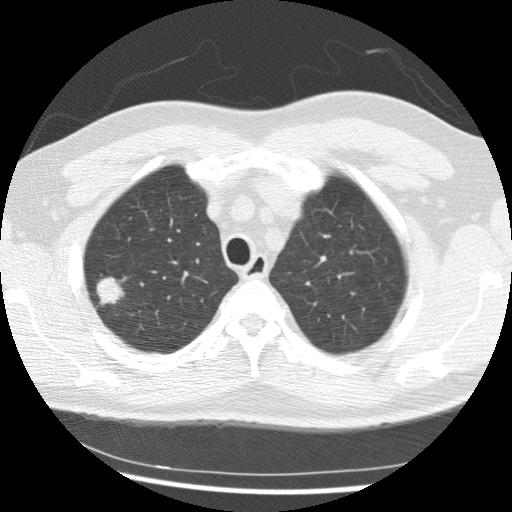
Low-dose screening chest CT, axial slice. First (baseline) screen. Lung window (W 1500 / L -600 HU). 512 × 512 image matrix. Male, age 56 years at enrolment. Current smoker at enrolment.
- Expert reader's lesion annotation, bounding box [x1, y1, x2, y2] px = [81, 272, 131, 315].
- Screening reader's record for this exam (one nodule recorded; not confirmed to be the boxed lesion): non-calcified nodule or mass ≥4 mm, right upper lobe, 19 × 15 mm, spiculated (stellate) margins, soft tissue attenuation.
- Later outcome: lung cancer diagnosed 291 days after this screen — non-small cell carcinoma, right upper lobe, poorly differentiated (G3), stage IIIB (AJCC 6th edition), 20 mm at pathology.